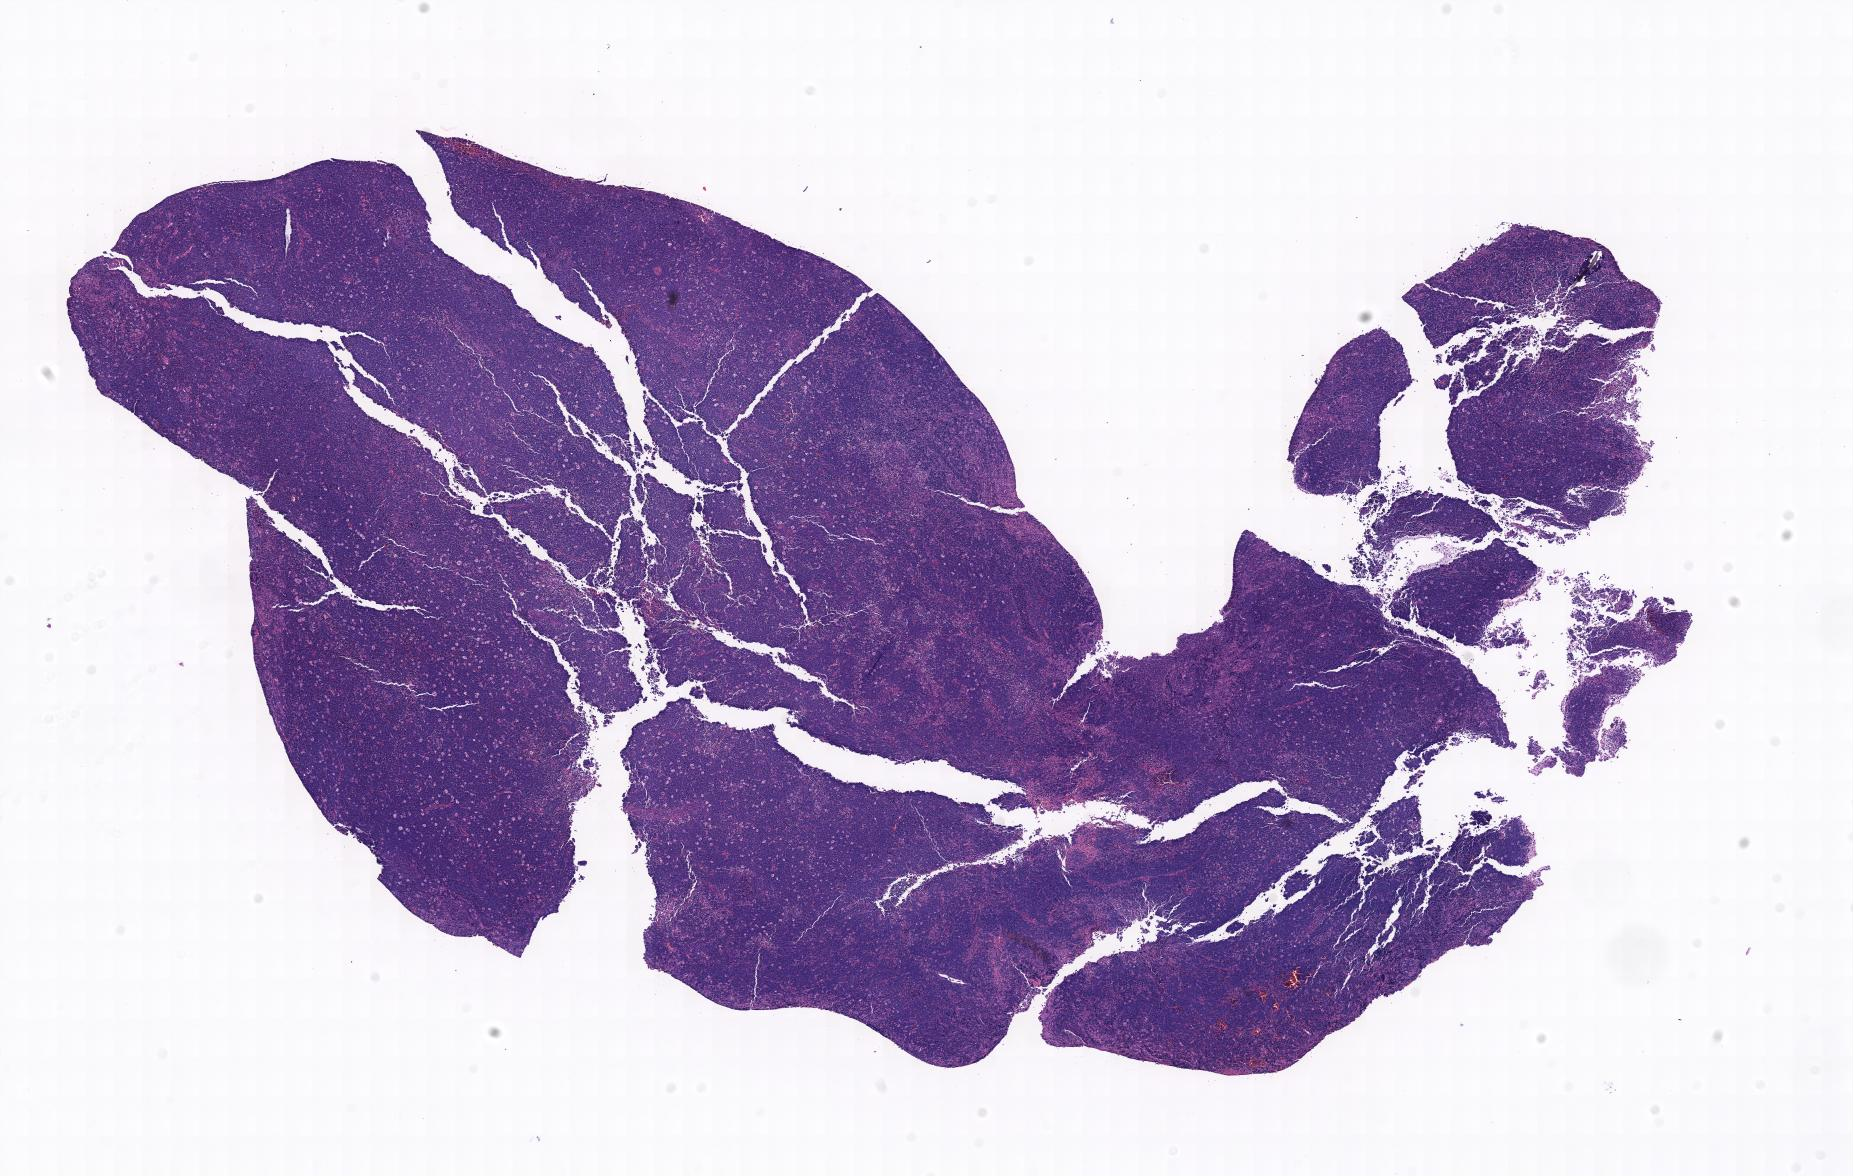
Haematoxylin and eosin whole-slide image — a low-resolution overview of the entire scanned area; tumor tissue; site: lymph node of head and neck. Male, age 5 years at initial diagnosis.
Diagnosis: Burkitt lymphoma, NOS.